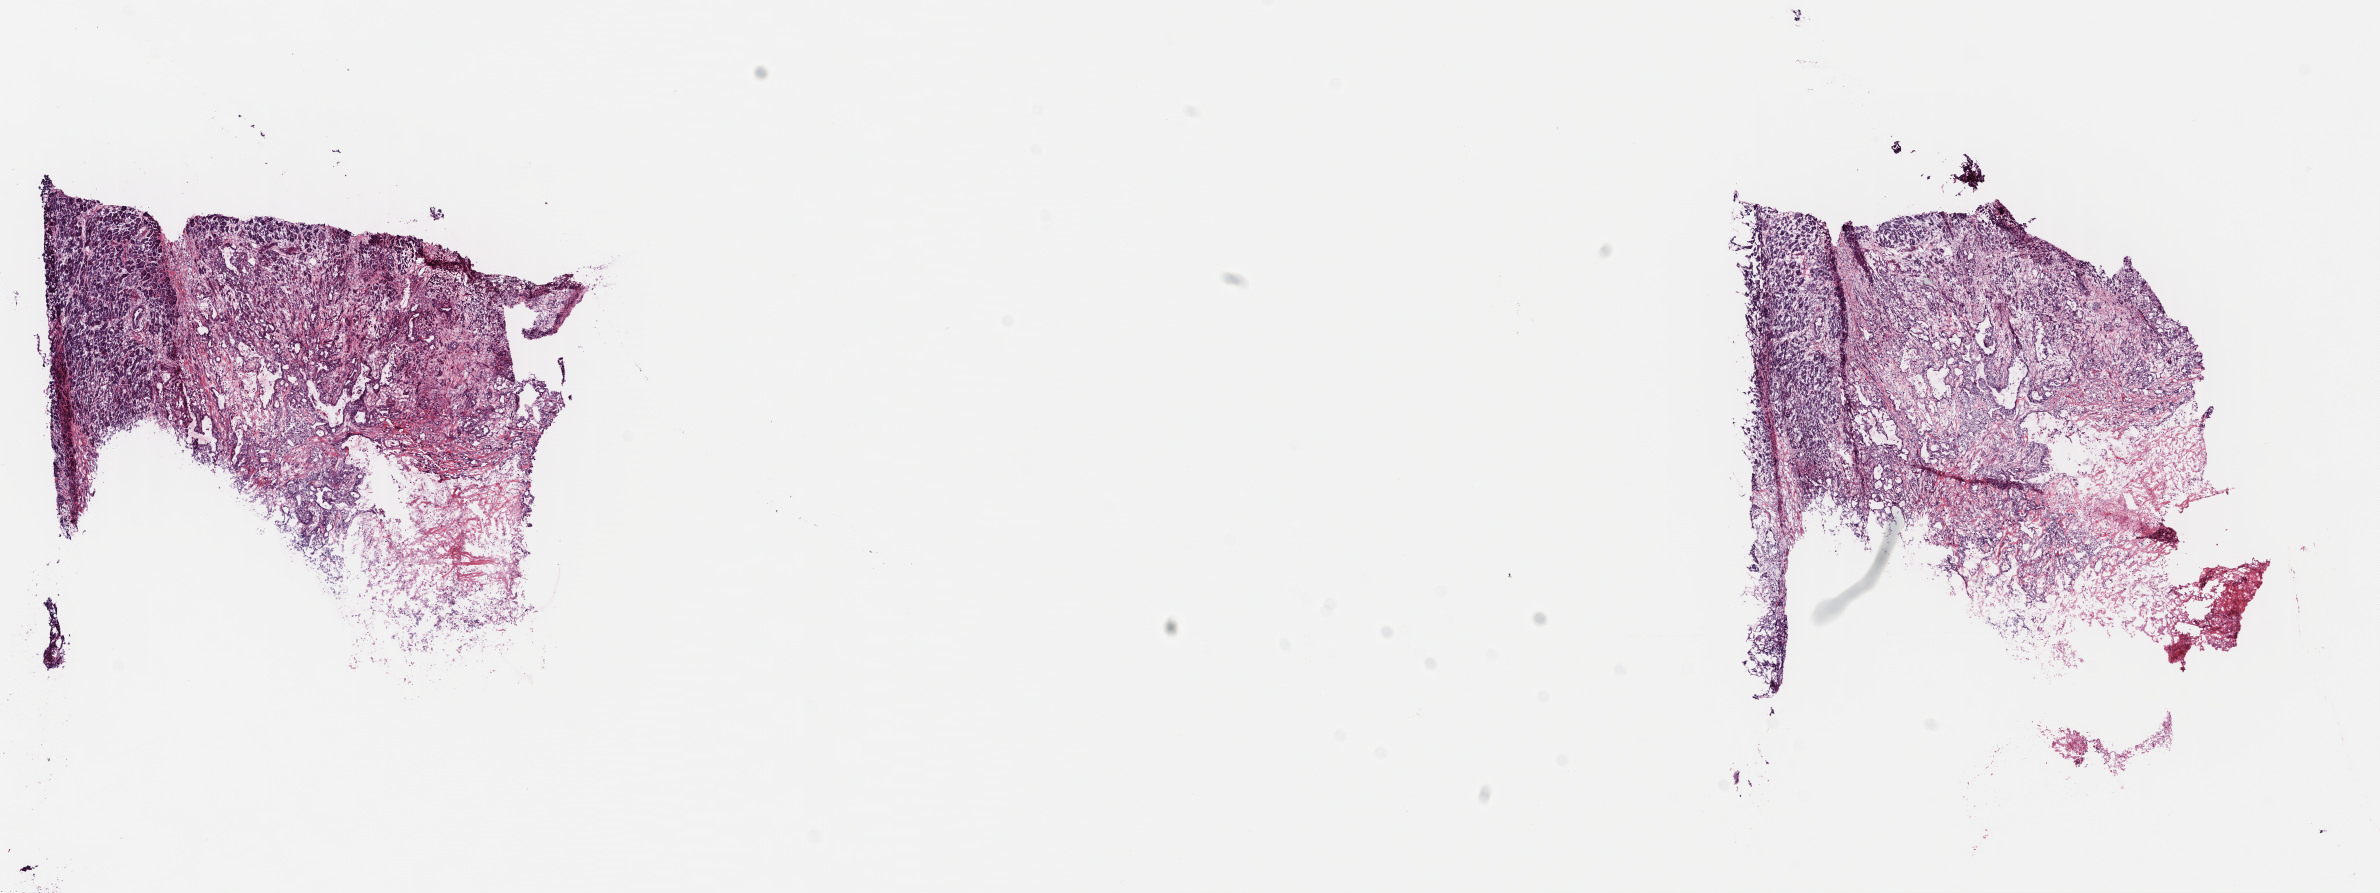
Hematoxylin and eosin (H&E) stained whole-slide image — low-resolution overview of the scanned area, about 18.7 x 7.0 mm. Frozen section. Primary tumour sample from the pancreas. Patient: female, age at initial diagnosis 77 years. Histologic grade: G2 (moderately differentiated). Slide review estimates, as recorded: tumour cells 100%, tumour nuclei 75%, normal cells 0%, stromal cells 0%, necrosis 0%. Infiltration values recorded for this section: lymphocyte infiltration 2%, monocyte infiltration 0%, neutrophil infiltration 0%.
• histologic diagnosis: Infiltrating duct carcinoma, NOS (head of pancreas)
• AJCC pathologic stage: IIB (7th edition)
• lymph nodes positive (case pathology): 4 of 26 examined
• TNM: T2 N1 MX